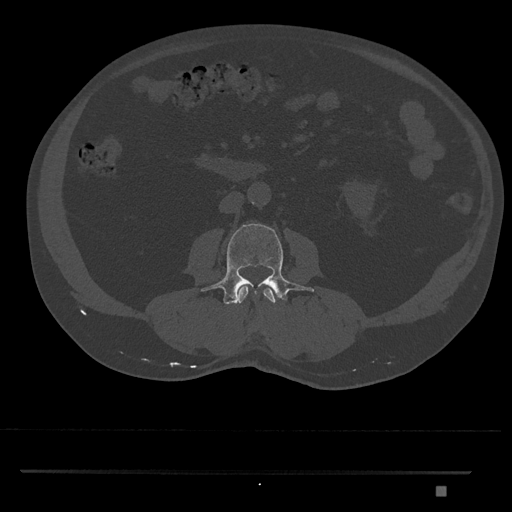
CT including the spine, one axial slice. Position 697 of 1134 along the scan axis. Reconstruction kernel Br40s/3. 120 kVp. Bone window (W 1800 / L 400 HU). 0.5 mm slice thickness. 512 × 512 image matrix, field of view 429 × 429 mm. Patient: male, 65 years. Case-level facts recorded for this patient, not image findings: primary cancer: prostate.
Outlined on this slice (semi-automatically segmented with operator editing):
- L2 vertebra: box from (x=237, y=285) to (x=276, y=304) px
- L3 vertebra: (x=202, y=223)–(x=314, y=305)